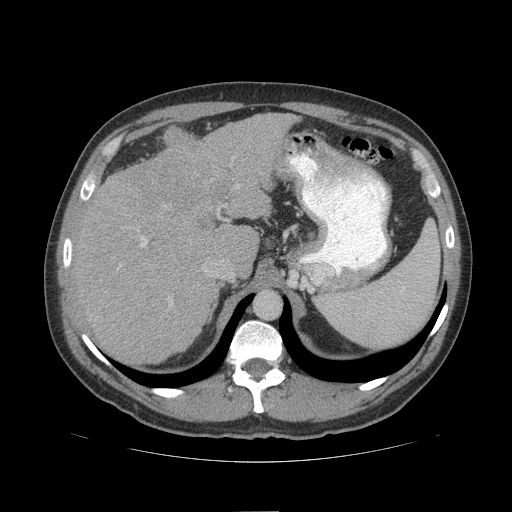
Contrast-enhanced abdominal CT (liver protocol), one axial slice. Slice 72 of 109 in the series (ordered by position). Reconstruction kernel STANDARD. 140 kVp. Soft-tissue window (W 400 / L 40 HU). 2.5 mm slice thickness. 512 × 512 image matrix, field of view 420 × 420 mm. Case-level facts recorded for this patient, not image findings: diagnosis: hepatocellular carcinoma (patient treated with transarterial chemoembolisation; whether this scan precedes or follows treatment is not stated here); TNM stage (as recorded): Stage-IIIB; Child-Pugh class: A; tumour nodularity: multinodular.
Annotated regions visible in this slice (semi-automatic segmentation, software-assisted and operator-edited):
- liver parenchyma outside the tumour (the mass and vessels are separate outlines, so this box may not span the whole liver): bounding box [x1, y1, x2, y2] px = [70, 112, 296, 362]
- mass: [122, 151, 231, 209]
- liver vessels: [118, 186, 239, 305]